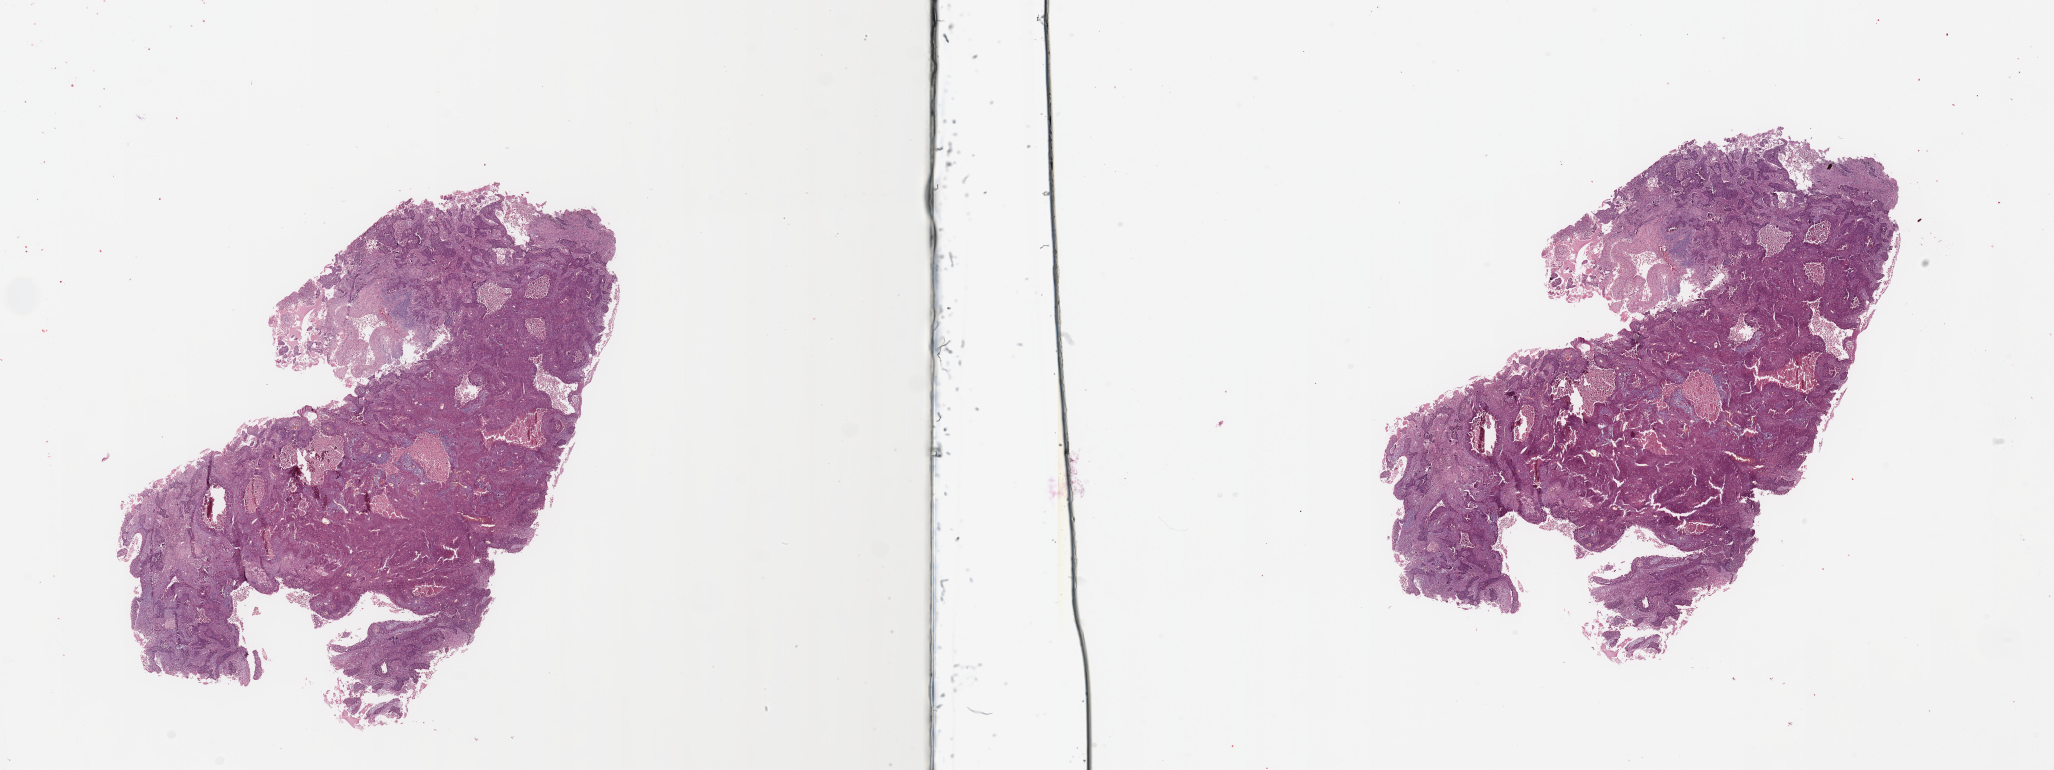
Hematoxylin and eosin (H&E) stained whole-slide image — a low-resolution overview of the entire scanned area, about 32.5 x 12.2 mm (slide scanned at 20x). Tumour tissue sample, sampled site: lung. Patient: male, age 64 years. Histologic grade: G2 (moderately differentiated). Slide review estimates, as recorded: tumour nuclei 75%, necrosis 15%.
Histologic diagnosis: Squamous cell carcinoma, NOS. AJCC pathologic stage: IIA.